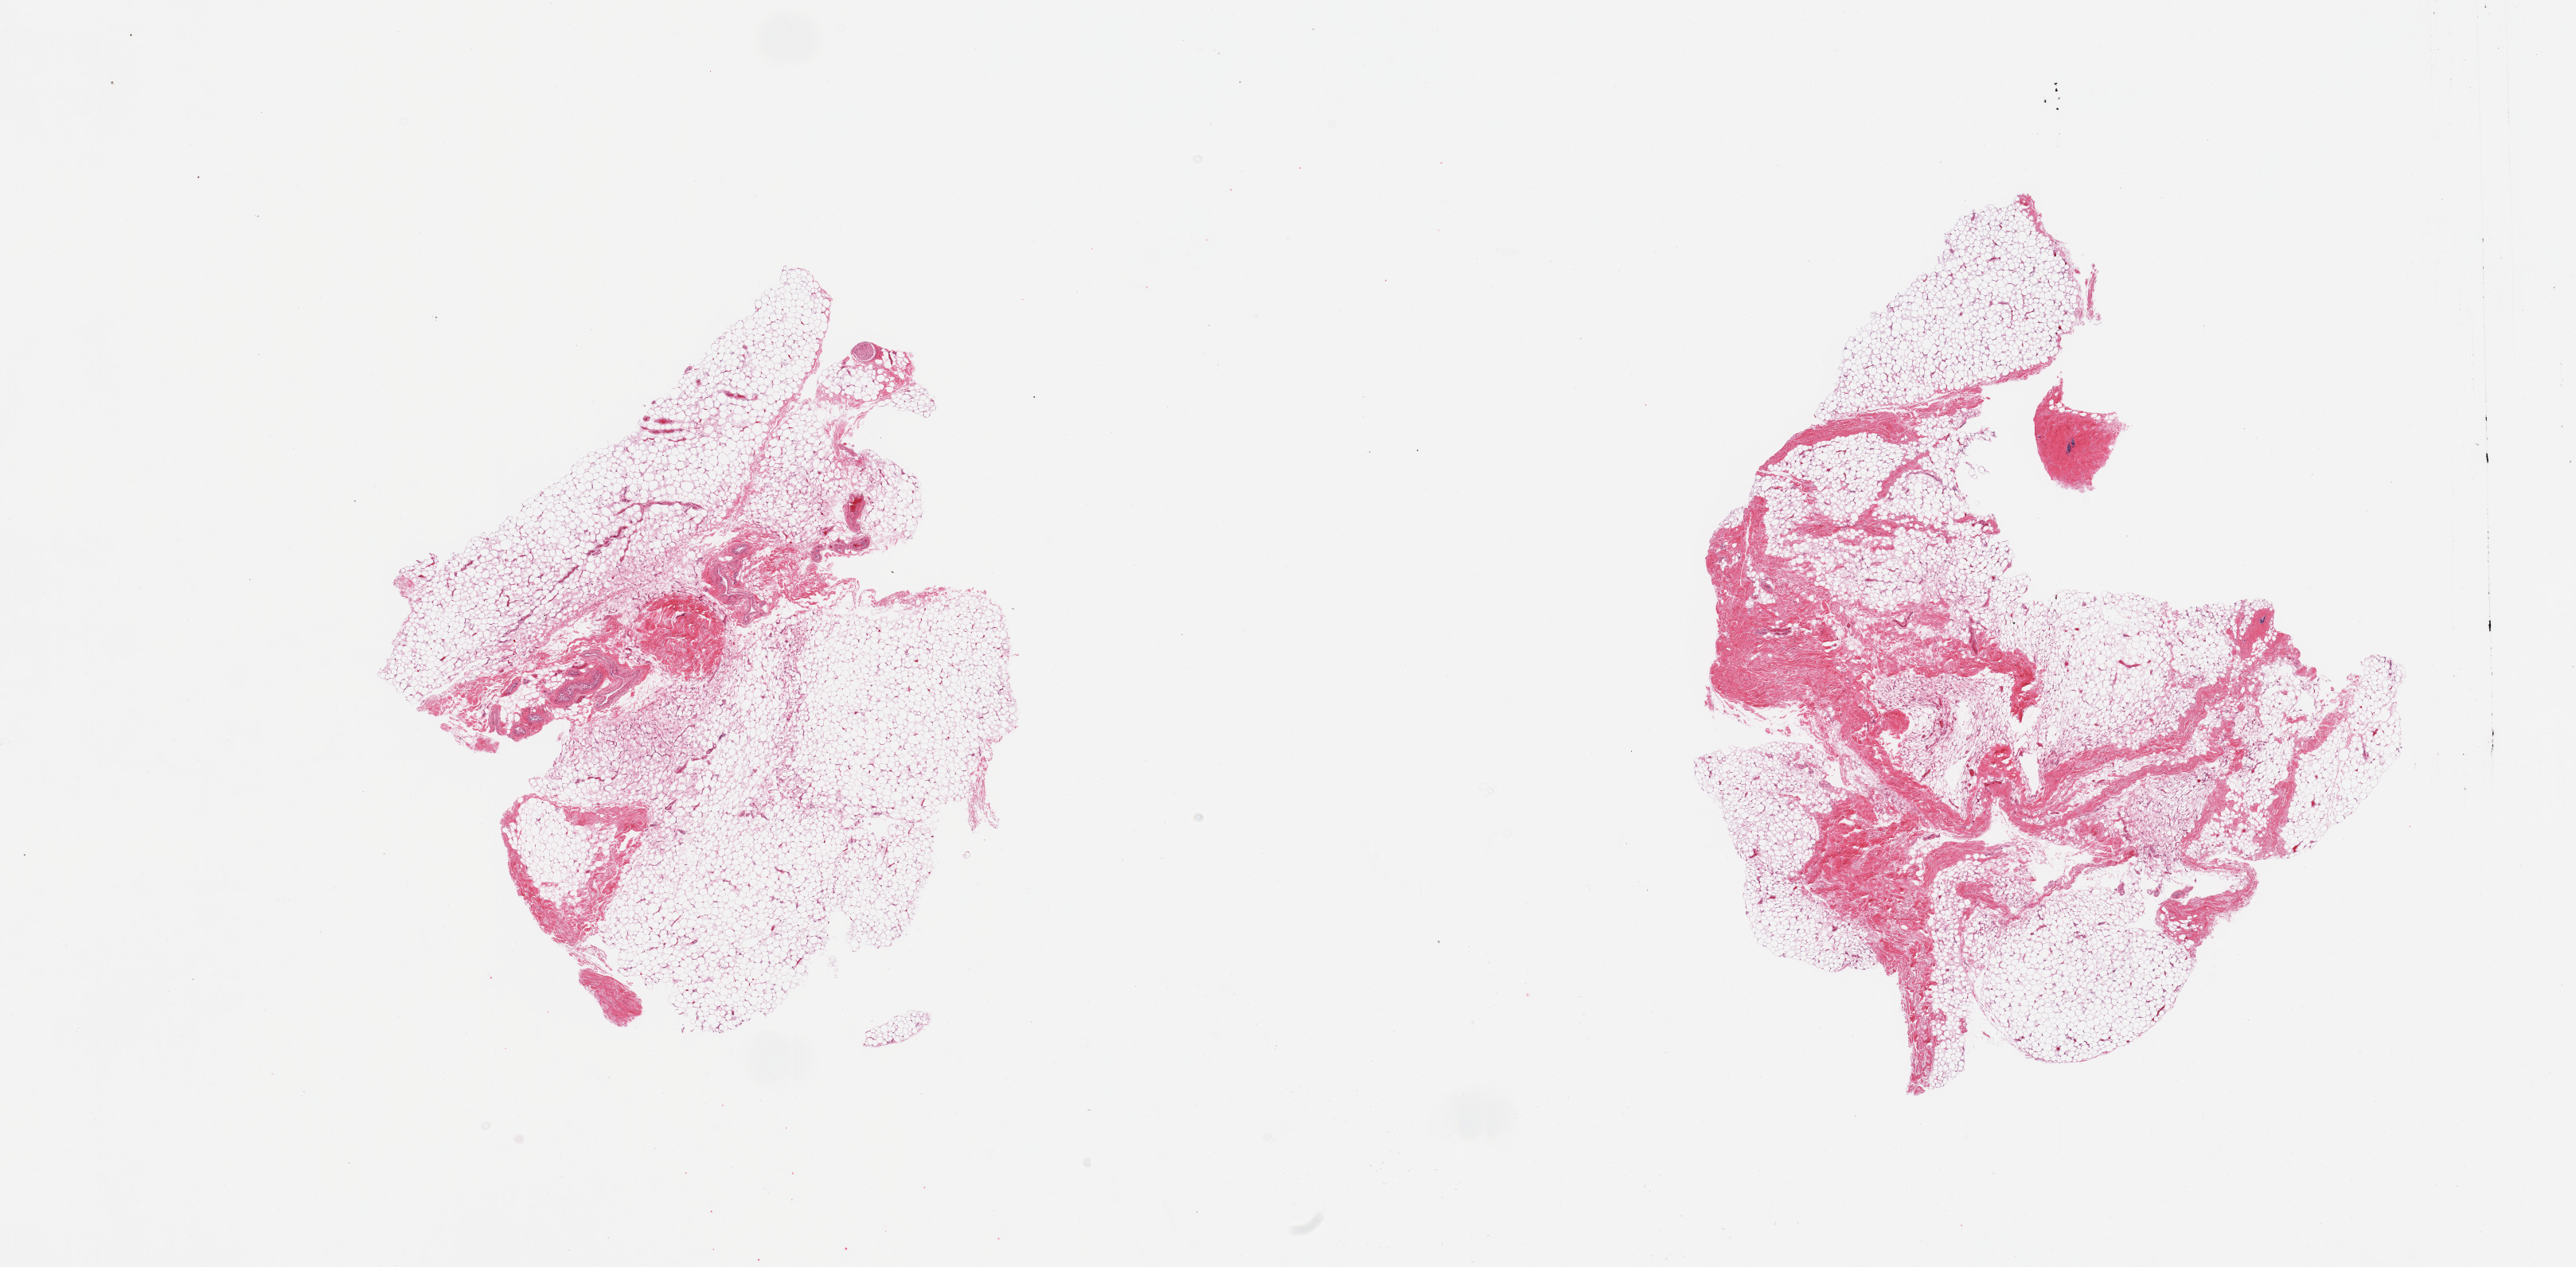
Digitized haematoxylin and eosin-stained section — whole scanned area (about 25.6 x 12.6 mm, from a 20x scan) shown as a low-resolution overview; PAXgene-fixed, paraffin-embedded tissue; target tissue: breast; tissue donor sample. Male donor.
• reviewer comment on this tissue sample: 2 pieces; fibrofatty tissue with 1 minute focus of ducts